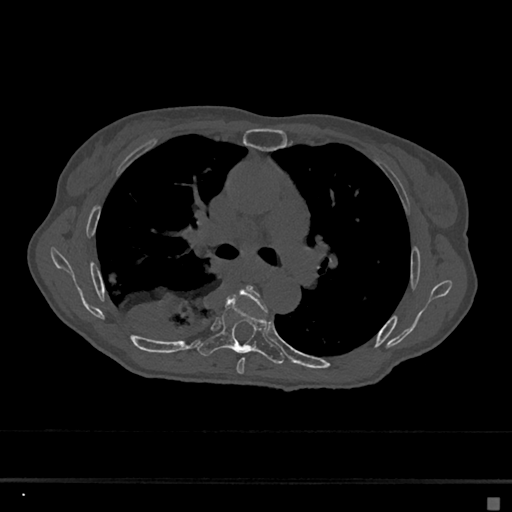
CT including the spine, one axial slice; slice 432 of 797 in the series (ordered by position); 120 kVp; bone window (W 1800 / L 400 HU); 512 × 512 image matrix, field of view 360 × 360 mm. Female patient, age 68 years. Case-level facts recorded for this patient, not image findings: primary cancer: renal.
Annotated regions visible in this slice (semi-automatic segmentation, software-assisted and operator-edited):
- T5 vertebra: bounding box (x1, y1, x2, y2) in pixels: (229, 285, 267, 375)
- T6 vertebra: (197, 297, 284, 364)